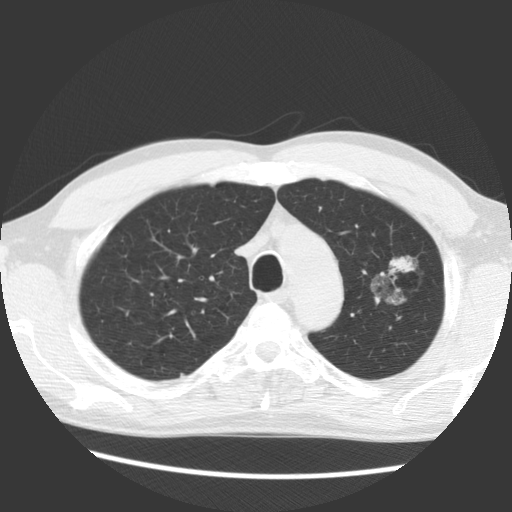
Axial slice from a low-dose chest CT screening exam. First (baseline) screen. Lung window (W 1500 / L -600 HU). 2.5 mm slice thickness. 512 × 512 image matrix, field of view 340 × 340 mm. Male participant, aged 61 years at enrolment. Former smoker at enrolment.
- Lesion marked by an expert reader, bounding box (x1, y1, x2, y2) in pixels: (351, 242, 436, 321).
- Reader record for this screening exam (exam-level; its link to the box is not recorded): non-calcified nodule or mass ≥4 mm, left upper lobe, 17 × 14 mm, soft tissue attenuation.